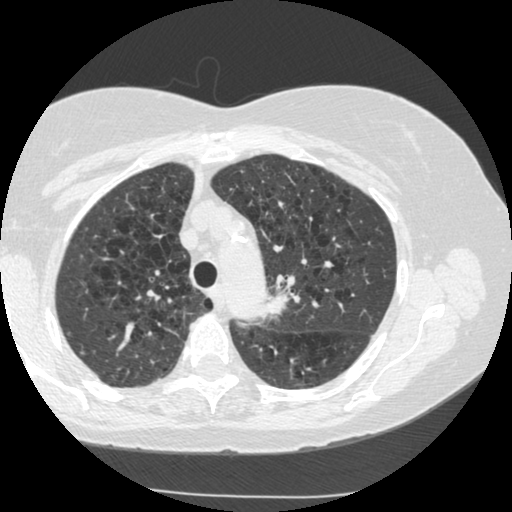
Axial slice from a low-dose chest CT screening exam; second annual screen; lung window (W 1500 / L -600 HU); 1.25 mm slice thickness; slice 194 of 249 in the series; 512 × 512 image matrix, field of view 320 × 320 mm. Female, age 70 years at enrolment.
- Expert-annotated lung lesion, bounding box <238,270,300,334> (left, top, right, bottom; pixels).
- Screening reader's record for this exam (one nodule recorded; not confirmed to be the boxed lesion): non-calcified nodule or mass ≥4 mm, left upper lobe, 15 × 13 mm, spiculated (stellate) margins, soft tissue attenuation, pre-existing on the prior screen: yes; interval growth: yes.
- Official screen result: positive, other.
- Later outcome: lung cancer diagnosed 360 days after this screen — neoplasm, malignant, left upper lobe, stage IIIB (AJCC 6th edition), 40 mm at pathology.